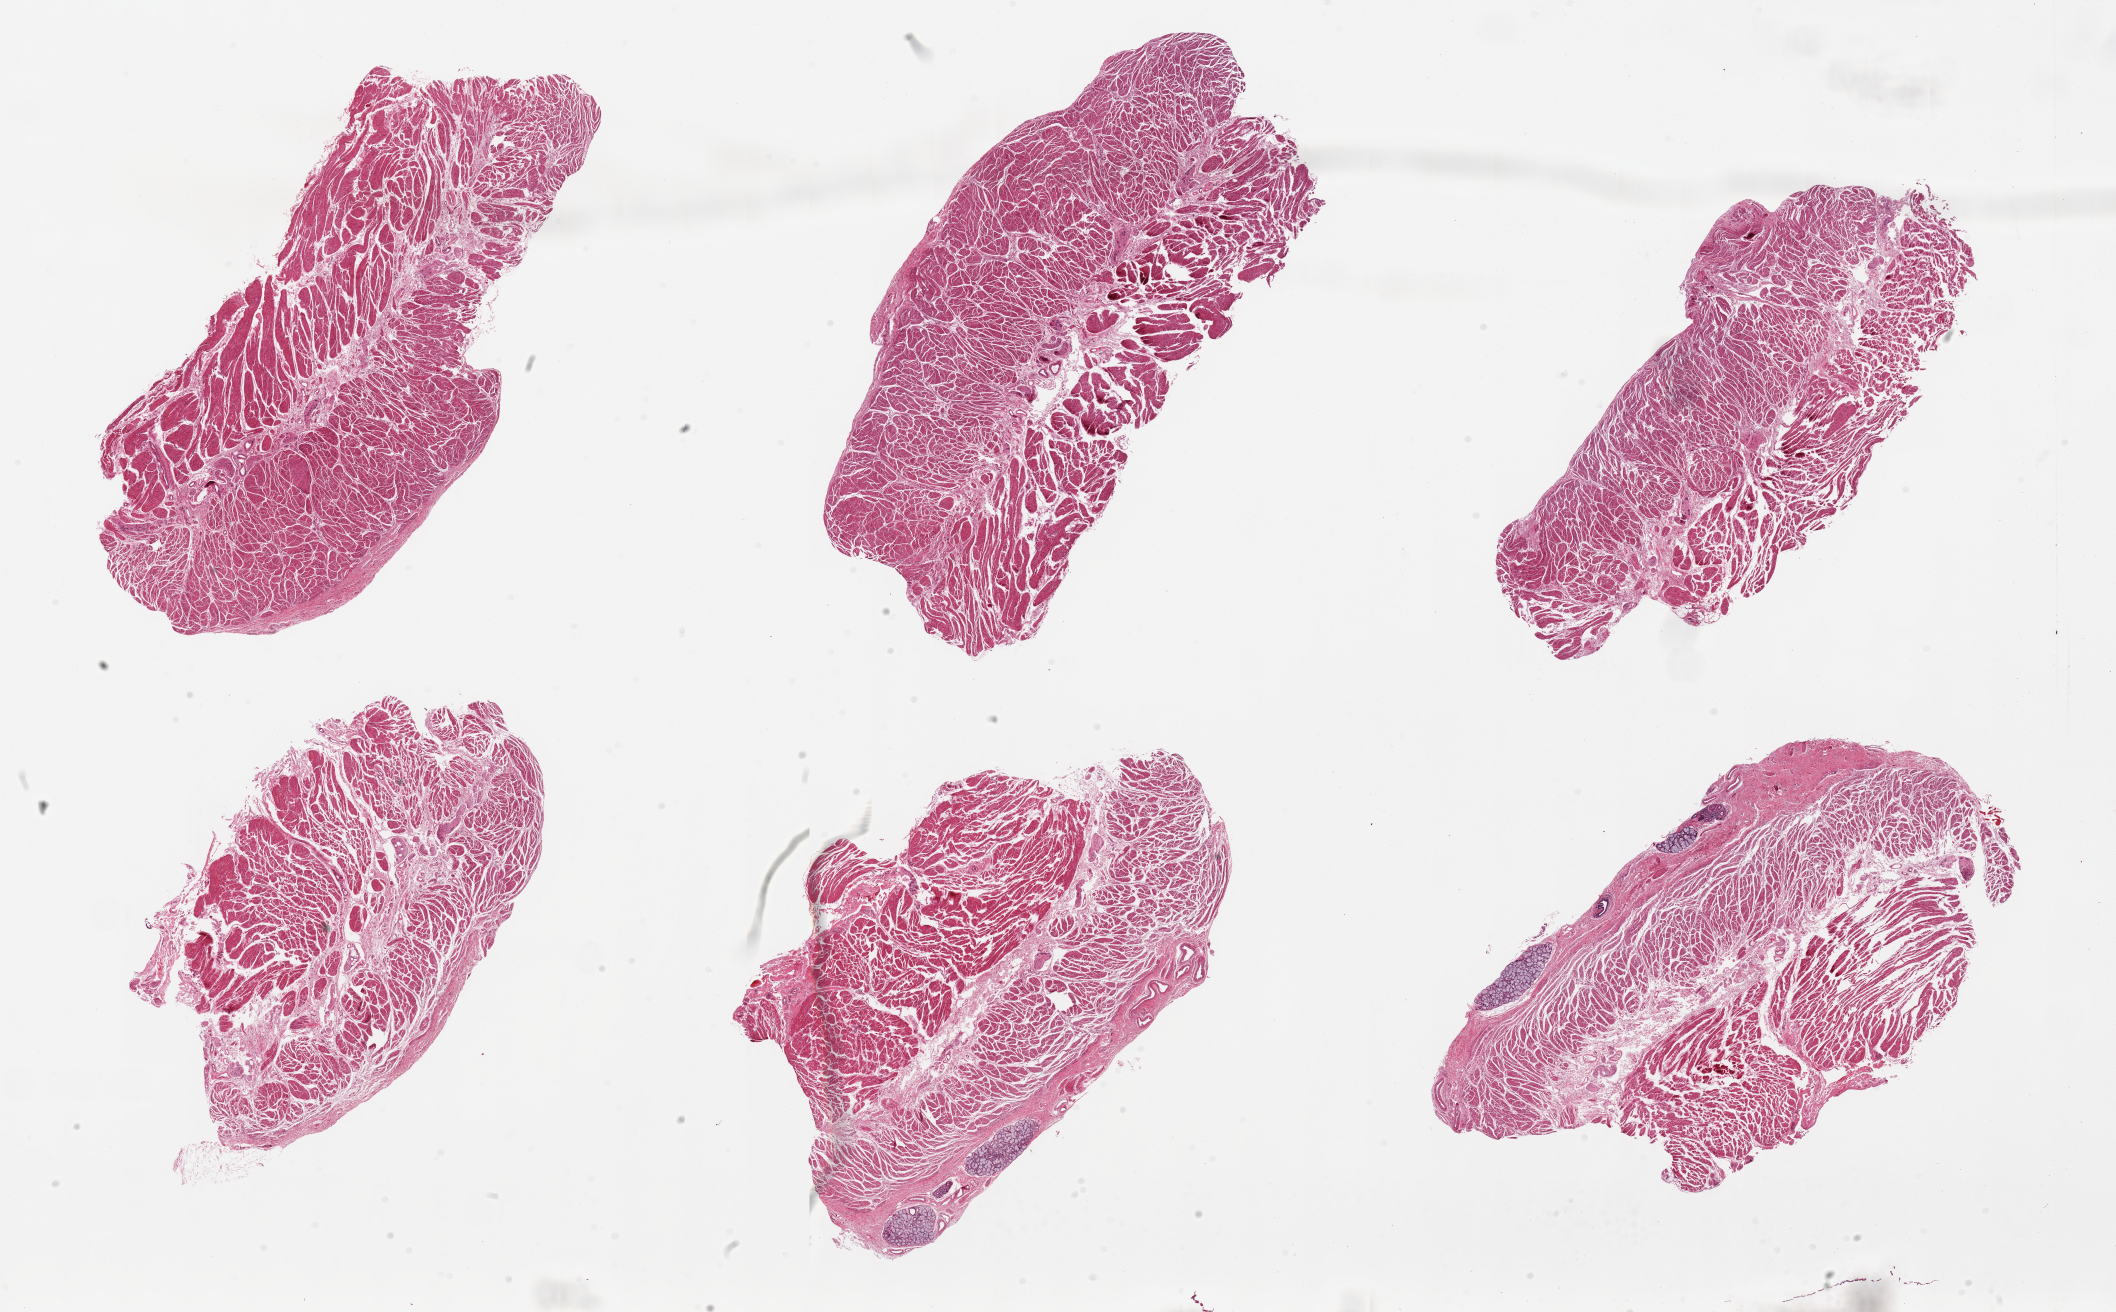
Haematoxylin and eosin whole-slide image, brightfield, shown as a low-resolution overview of the whole scanned area (about 33.5 x 20.8 mm, from a 20x scan). PAXgene-fixed, paraffin-embedded tissue. Sampled site (target tissue): gastroesophageal junction. Donor tissue sample.
Pathologist's review note for this sample: 6 pieces, up to 11x6mm; all mscularis, good specimens; focal submucosal glands in several sections.